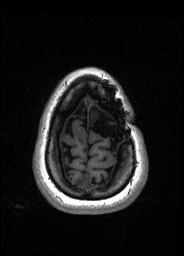
Pre-operative brain MRI before brain-tumour surgery, one axial slice. Slice 33 of 176 in the series (ordered by position). T1-weighted post-contrast. 1 mm slice thickness. 184 × 256 image matrix, field of view 180 × 250 mm. From the clinical record (not read from this slice): histopathology: Oligodendroglioma; WHO grade: 2; IDH mutation: yes.
Annotated regions visible in this slice (outlined manually by an expert reader):
- tumour: bounding box (x1, y1, x2, y2) in pixels: (88, 111, 99, 126)